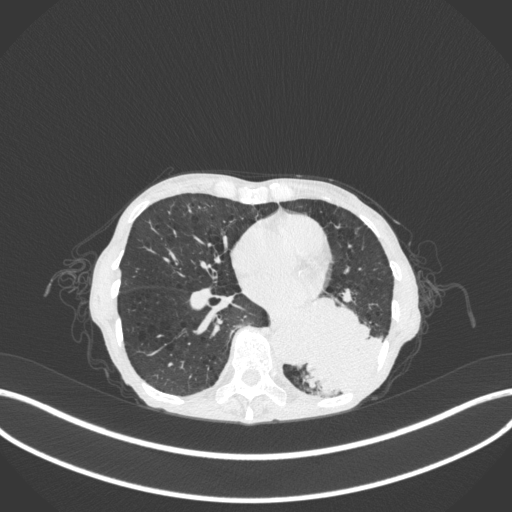
Chest CT, one axial slice; slice 117 of 347 in the series (ordered by position); reconstruction kernel B31f; 120 kVp; lung window (W 1500 / L -600 HU); 1 mm slice thickness; 512 × 512 image matrix. Patient: female, 70 years. Case-level facts recorded for this patient, not image findings: clinical TNM (as recorded): T3 N0 M0; histopathological grade: G3.
Outlined on this slice (bounding box drawn by a radiologist):
- lung tumour (recorded histology: small cell carcinoma): box from (x=298, y=290) to (x=390, y=394) px